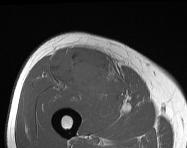
MRI of an extremity soft-tissue mass, one axial slice; position 72 of 114 along the scan axis; MR volume resampled by the dataset authors to the PET/CT grid (not the native acquisition matrix); 3.27 mm slice thickness; 187 × 148 image matrix, field of view 183 × 145 mm. Male patient. From the clinical record (not read from this slice): histological type: pleiomorphic leiomyosarcoma; grade: intermediate; site of the primary tumour: right thigh.
Annotated regions visible in this slice (expert contour drawn on MRI and transferred to this co-registered scan by the dataset authors):
- gross tumour volume including surrounding oedema: bounding box <54,49,112,96> (left, top, right, bottom; pixels)
- gross tumour volume (mass): <54,50,112,94>